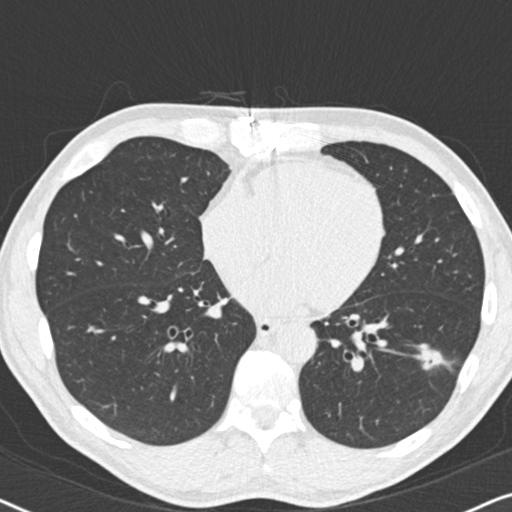
Low-dose screening chest CT, axial slice. Second annual screen. Lung window (W 1500 / L -600 HU). Standard (soft-tissue) reconstruction kernel (B30f). 120 kVp. Male, age 59 years at enrolment.
Expert reader's lesion annotation, bounding box [x1, y1, x2, y2] px = [411, 335, 464, 383]. The screening reader recorded 2 non-calcified nodules or masses ≥4 mm on this exam; which of them this box marks is not recorded. Official screen result: positive, other. Later outcome: lung cancer diagnosed 484 days after this screen (after the third annual screen) — adenocarcinoma, NOS, left lower lobe, poorly differentiated (G3), stage IA (AJCC 6th edition), 20 mm at pathology.